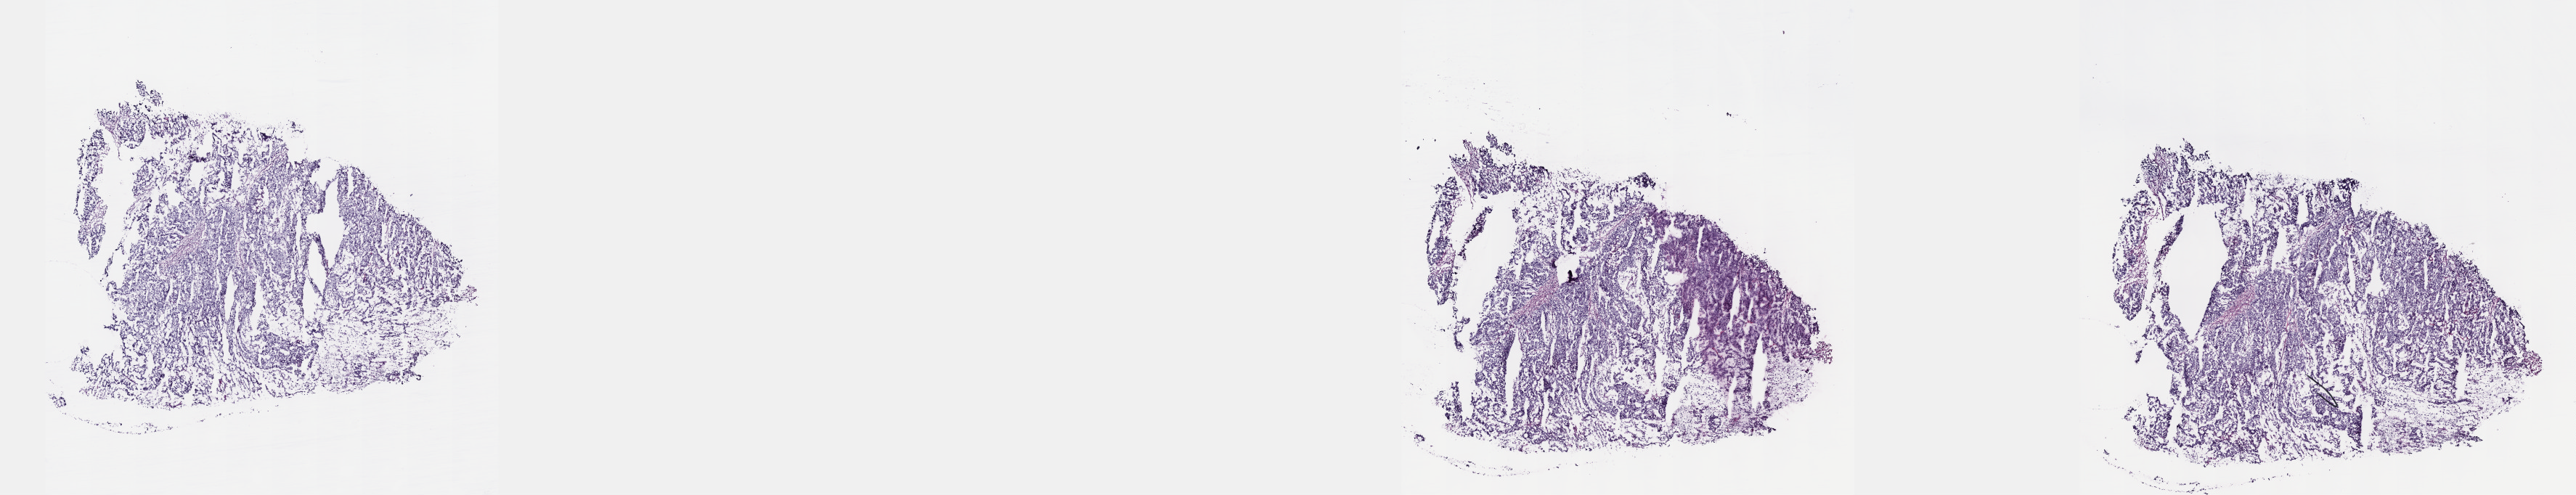
Whole-slide histology image, H&E, low-resolution overview of the scanned area, about 28.7 x 5.5 mm, frozen section from the top of the tissue portion, primary tumour sample from the testis. Male, age 18 years at initial diagnosis. Pathologist review of this section (percent, as recorded): tumour cells 90%, tumour nuclei 95%, normal cells 0%, stromal cells 10%, necrosis 0%. Inflammatory infiltration, as recorded: lymphocyte infiltration 0%, monocyte infiltration 0%, neutrophil infiltration 0%.
* AJCC pathologic stage: IS (7th edition)
* pathologic diagnosis: Embryonal carcinoma, NOS